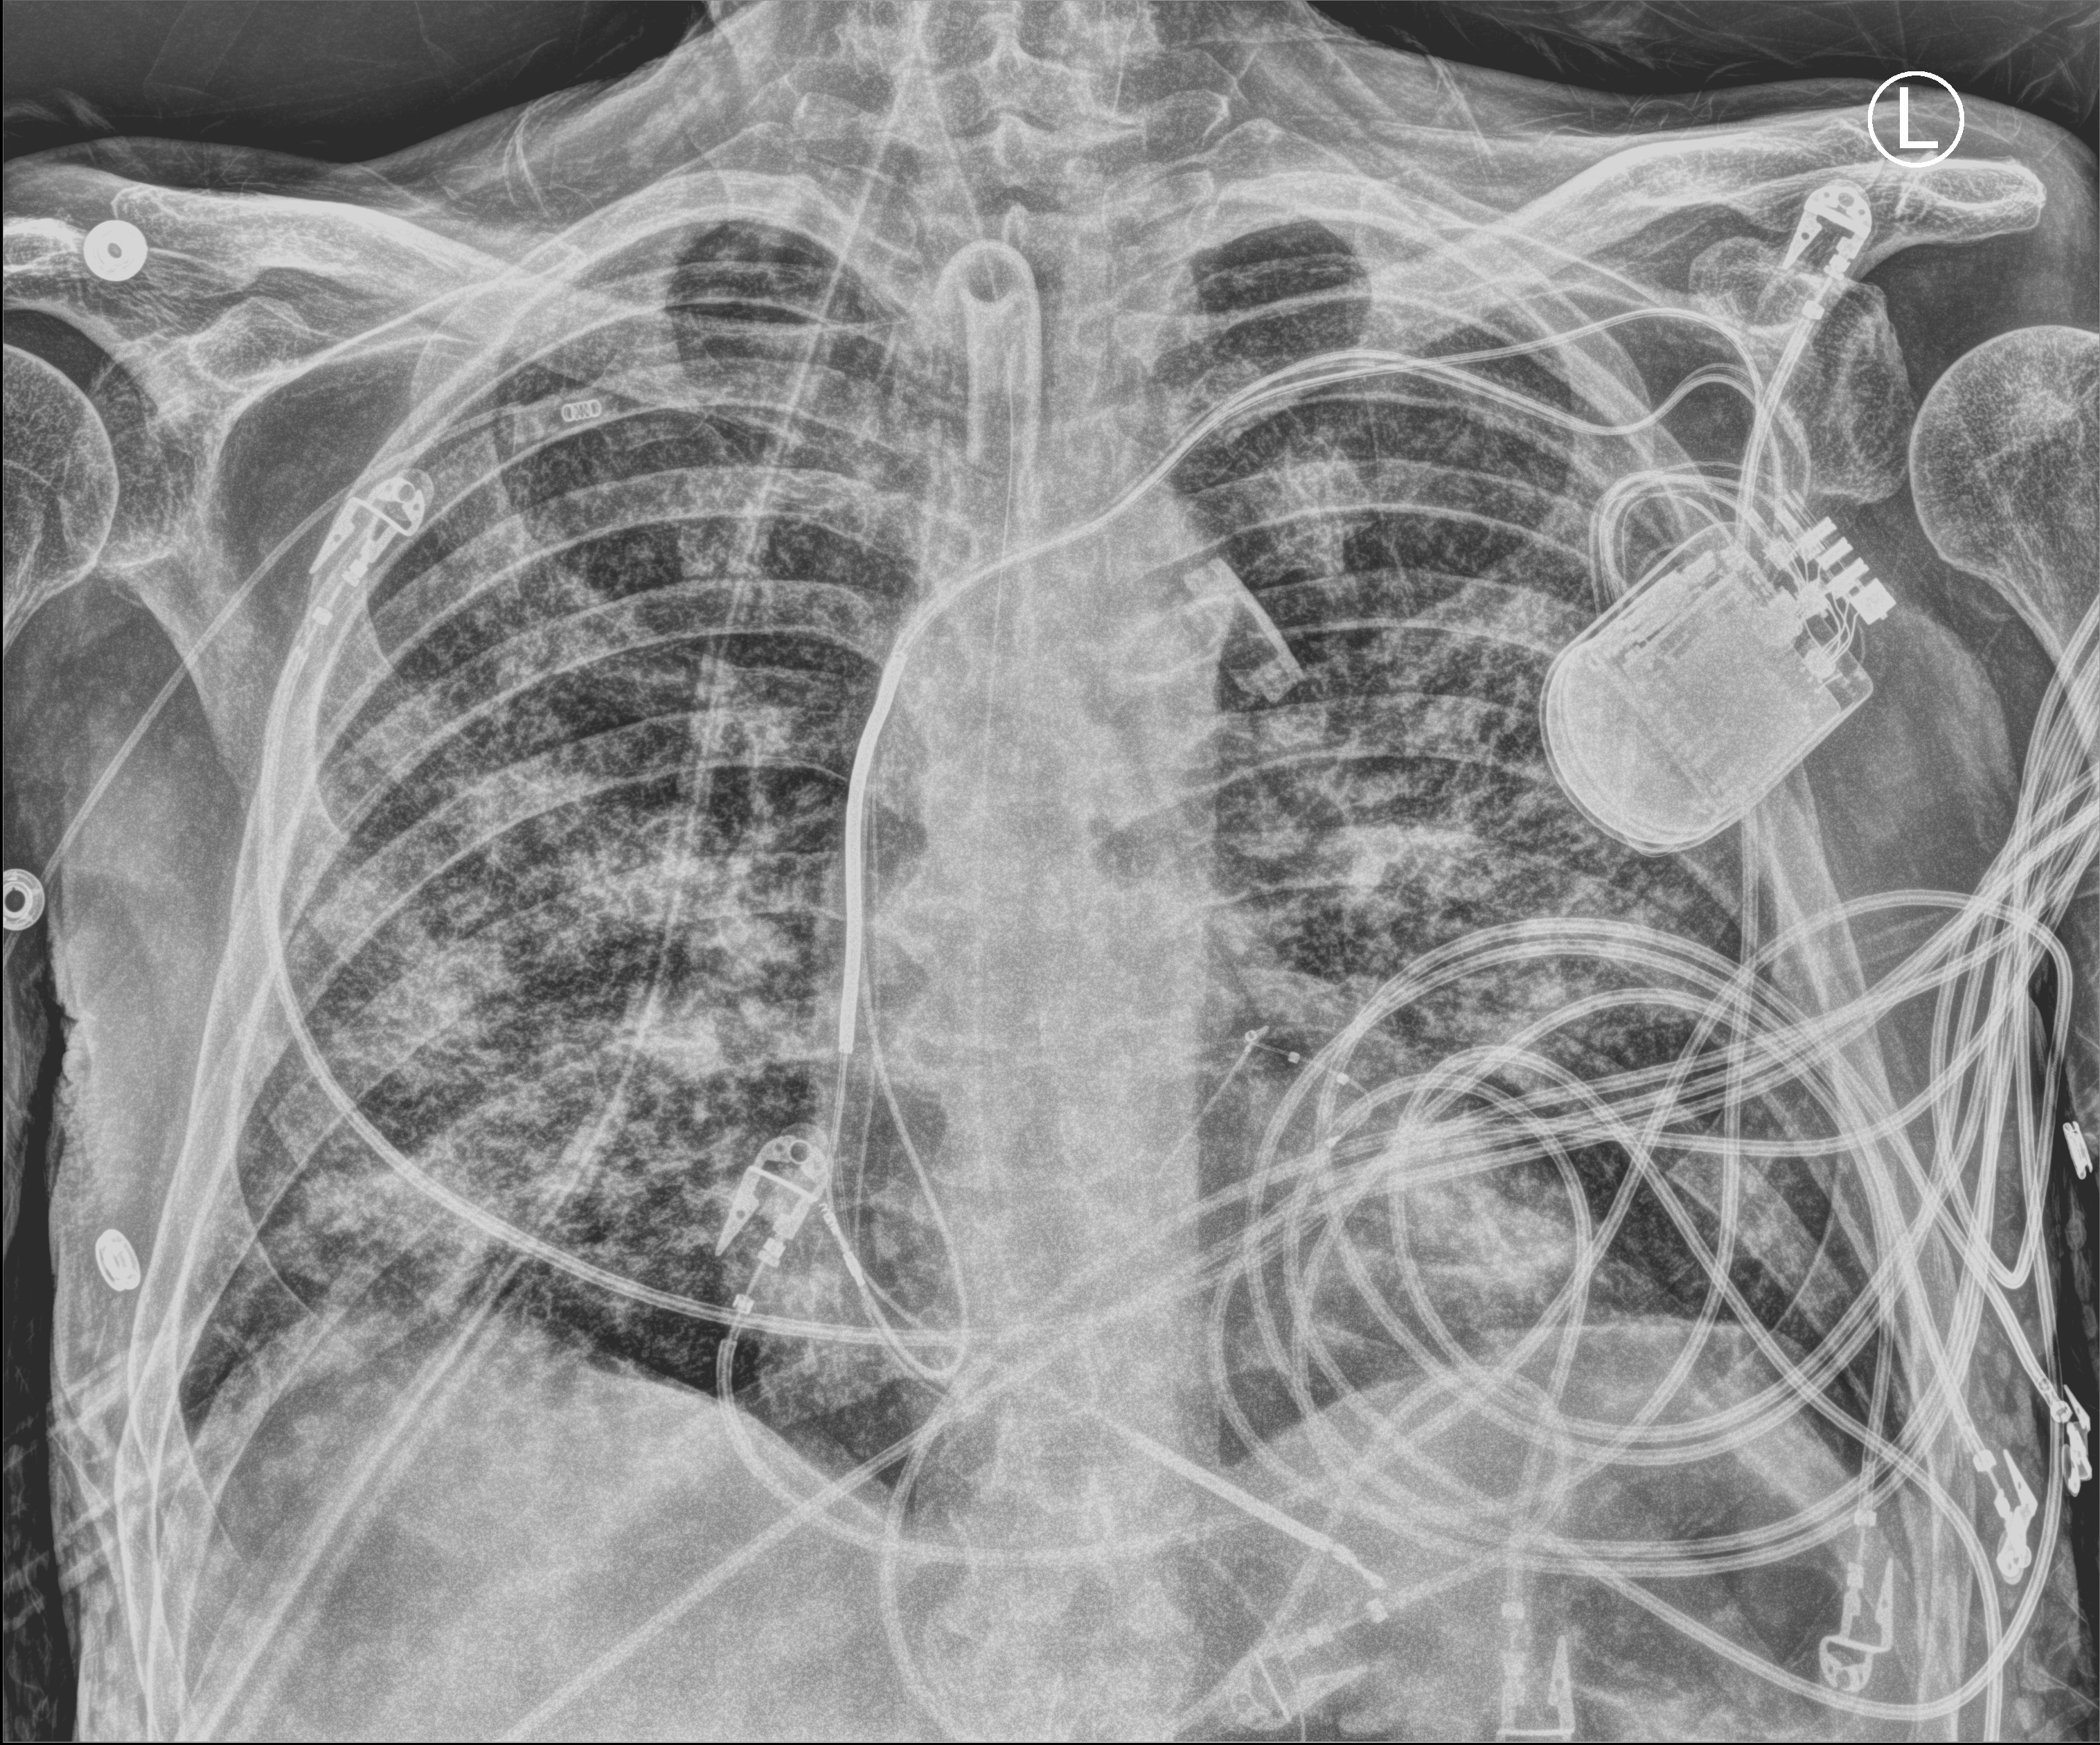
Bedside chest radiograph (computed radiography); anteroposterior (AP) projection. Male patient hospitalised with COVID-19, age 60–74 years.
From the hospital-stay record, not from the radiograph (when in the stay this image was taken is not recorded): length of hospital stay: 36 days; smoking status (admission record): former; other chronic lung disease (admission record): no.